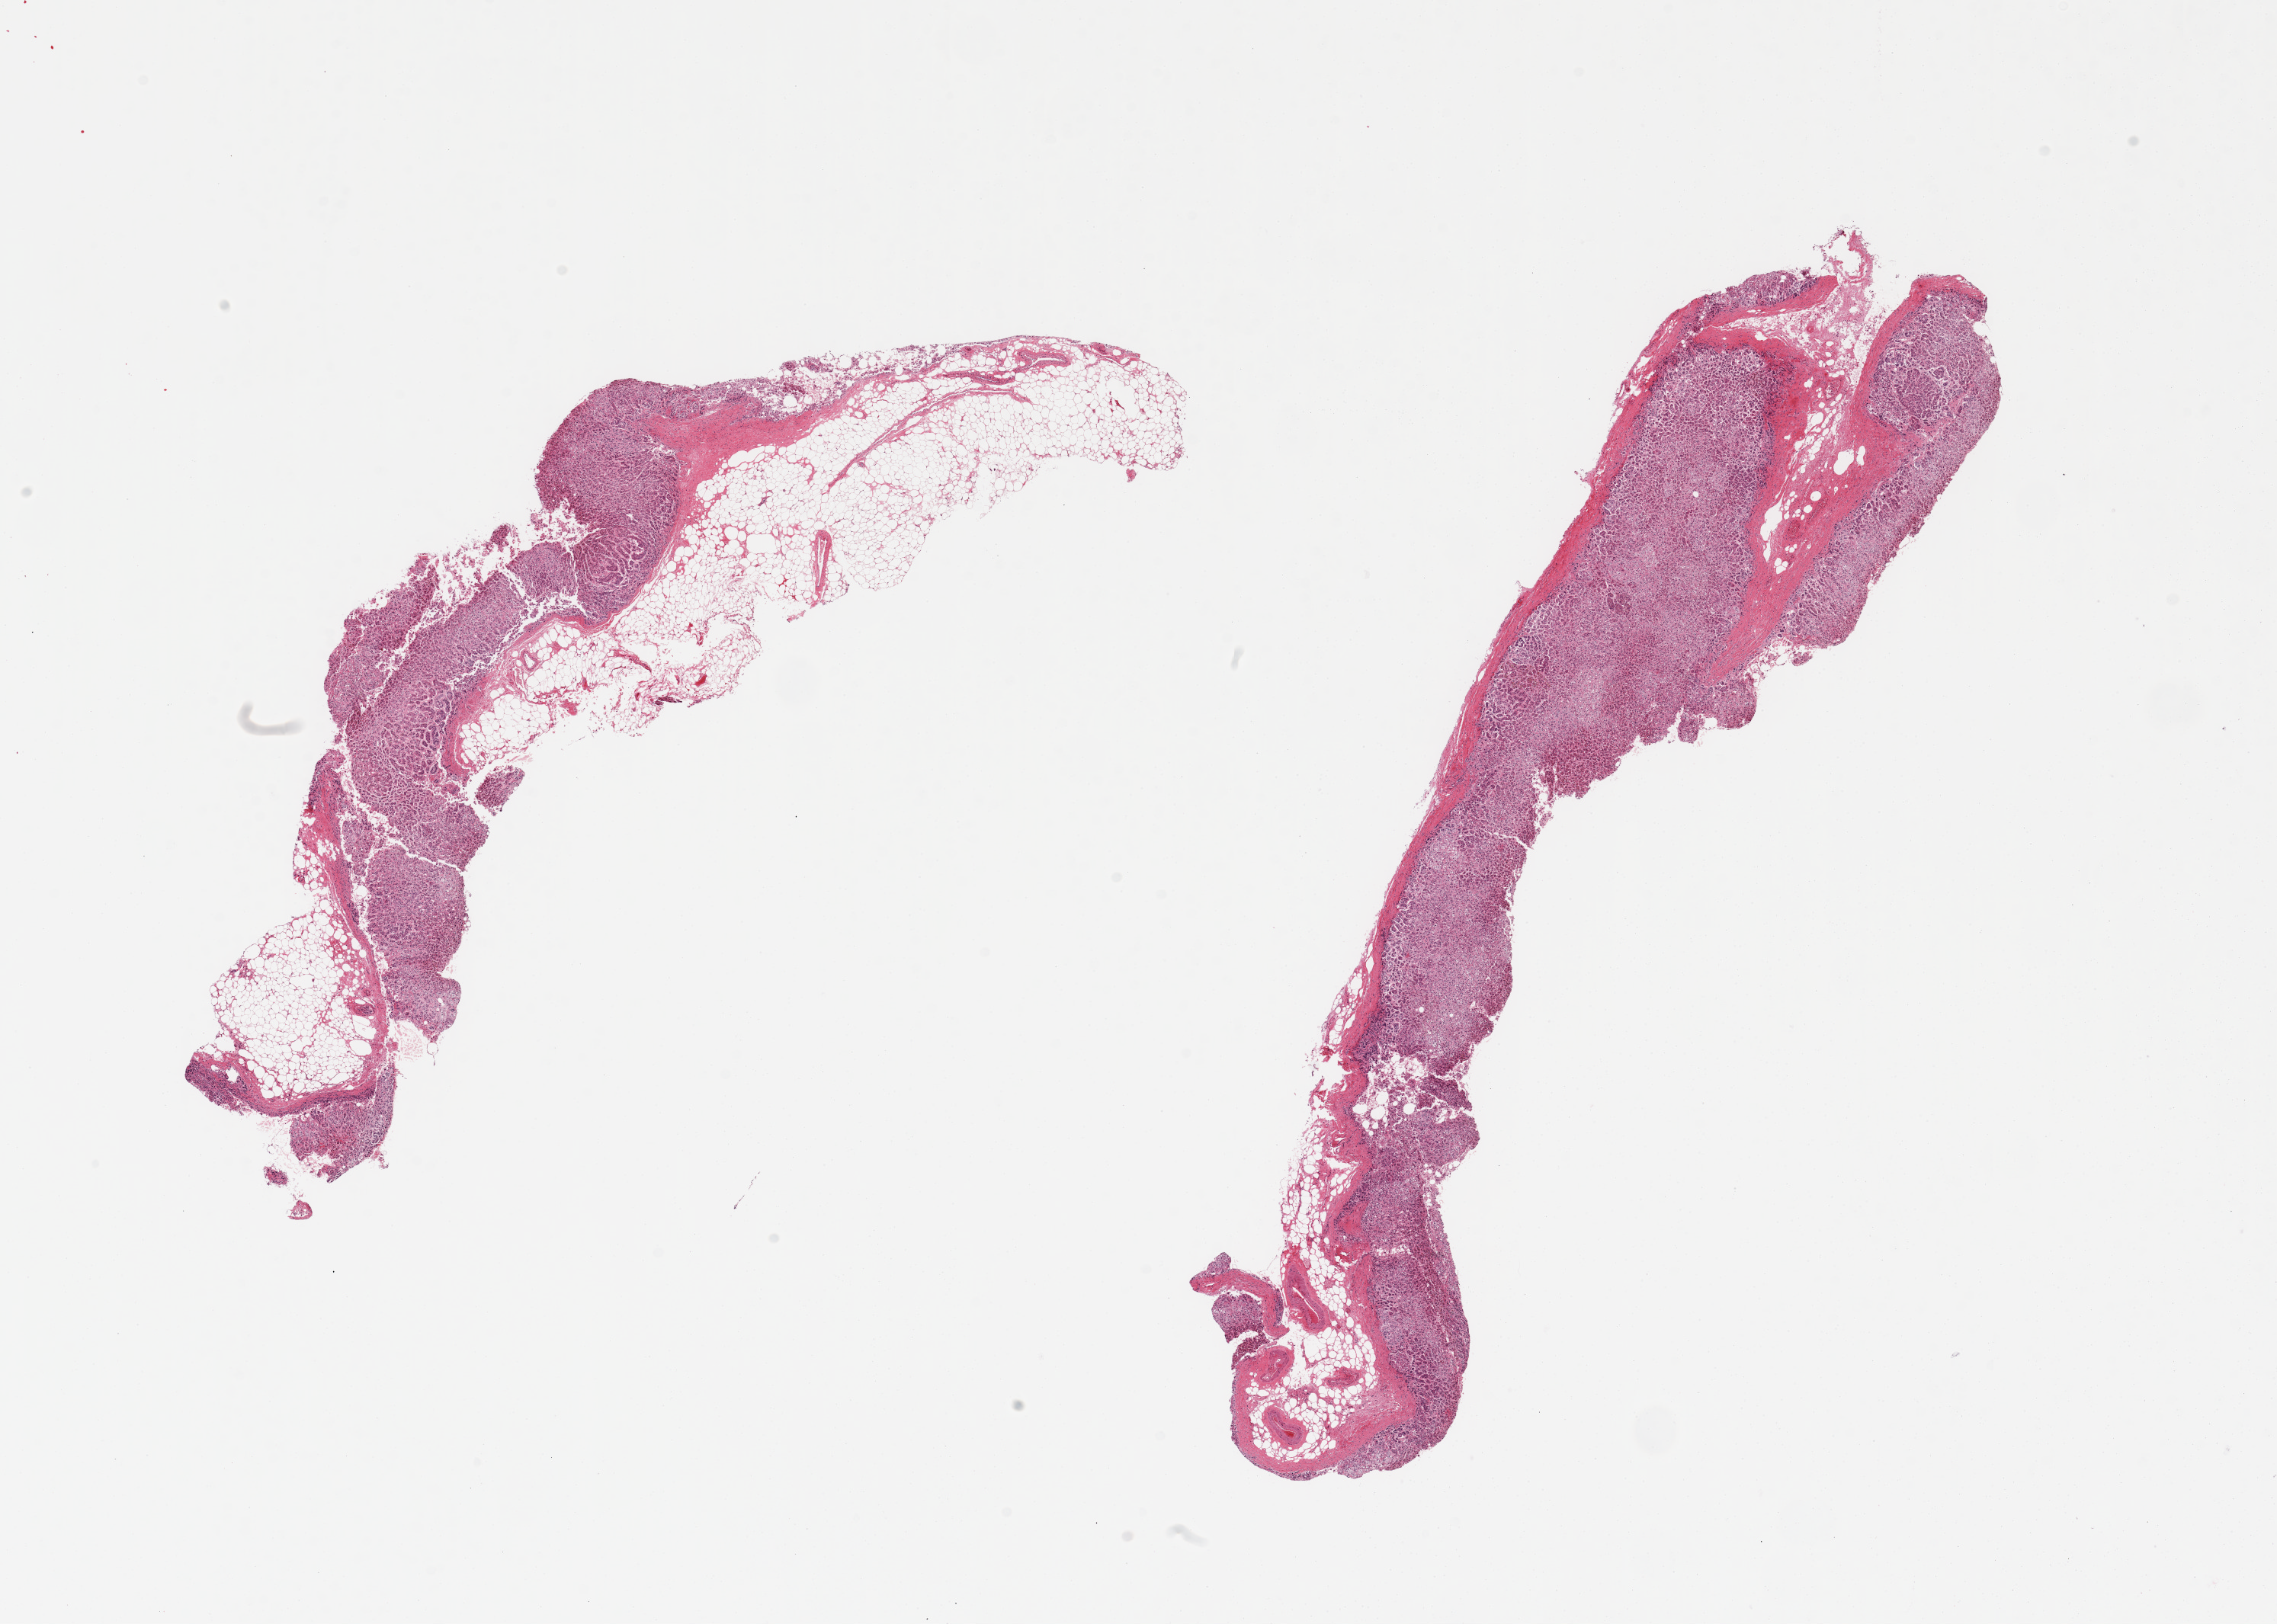
Digitized haematoxylin and eosin-stained section, shown as a low-resolution overview of the whole scanned area (about 23.6 x 16.9 mm). PAXgene-fixed, paraffin-embedded tissue. Target tissue: adrenal gland. Tissue donor sample. Donor: male.
Pathologist's review note for this sample: 2 pieces, cortex is ~60% total tissue (delineated0 rest is adherent/interstitial fat.